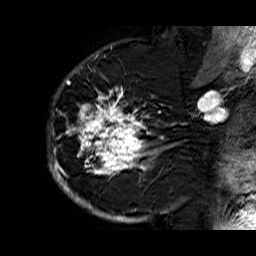
Breast MRI (dynamic contrast-enhanced), one sagittal slice. Position 44 of 60 along the scan axis. Dynamic contrast-enhanced series, time point 2 of 6 at this slice position (early post-contrast). 1.5 T. TE 6.3 ms, TR 32.9 ms. 4 mm slice thickness. 256 × 256 image matrix, field of view 200 × 200 mm. Female patient. From the clinical record (not read from this slice): setting: breast cancer imaged before/during neoadjuvant chemotherapy; receptor status: HR-positive, HER2-negative.
Outlined on this slice (semi-automatic segmentation, software-assisted and operator-edited):
- analysis volume of interest (the breast-tissue region the enhancement analysis was run in; not a lesion): bounding box <47,74,176,210> (left, top, right, bottom; pixels)
- tumour enhancement mask (voxels above the 100 % enhancement threshold inside the analysis volume of interest): <48,74,173,210>